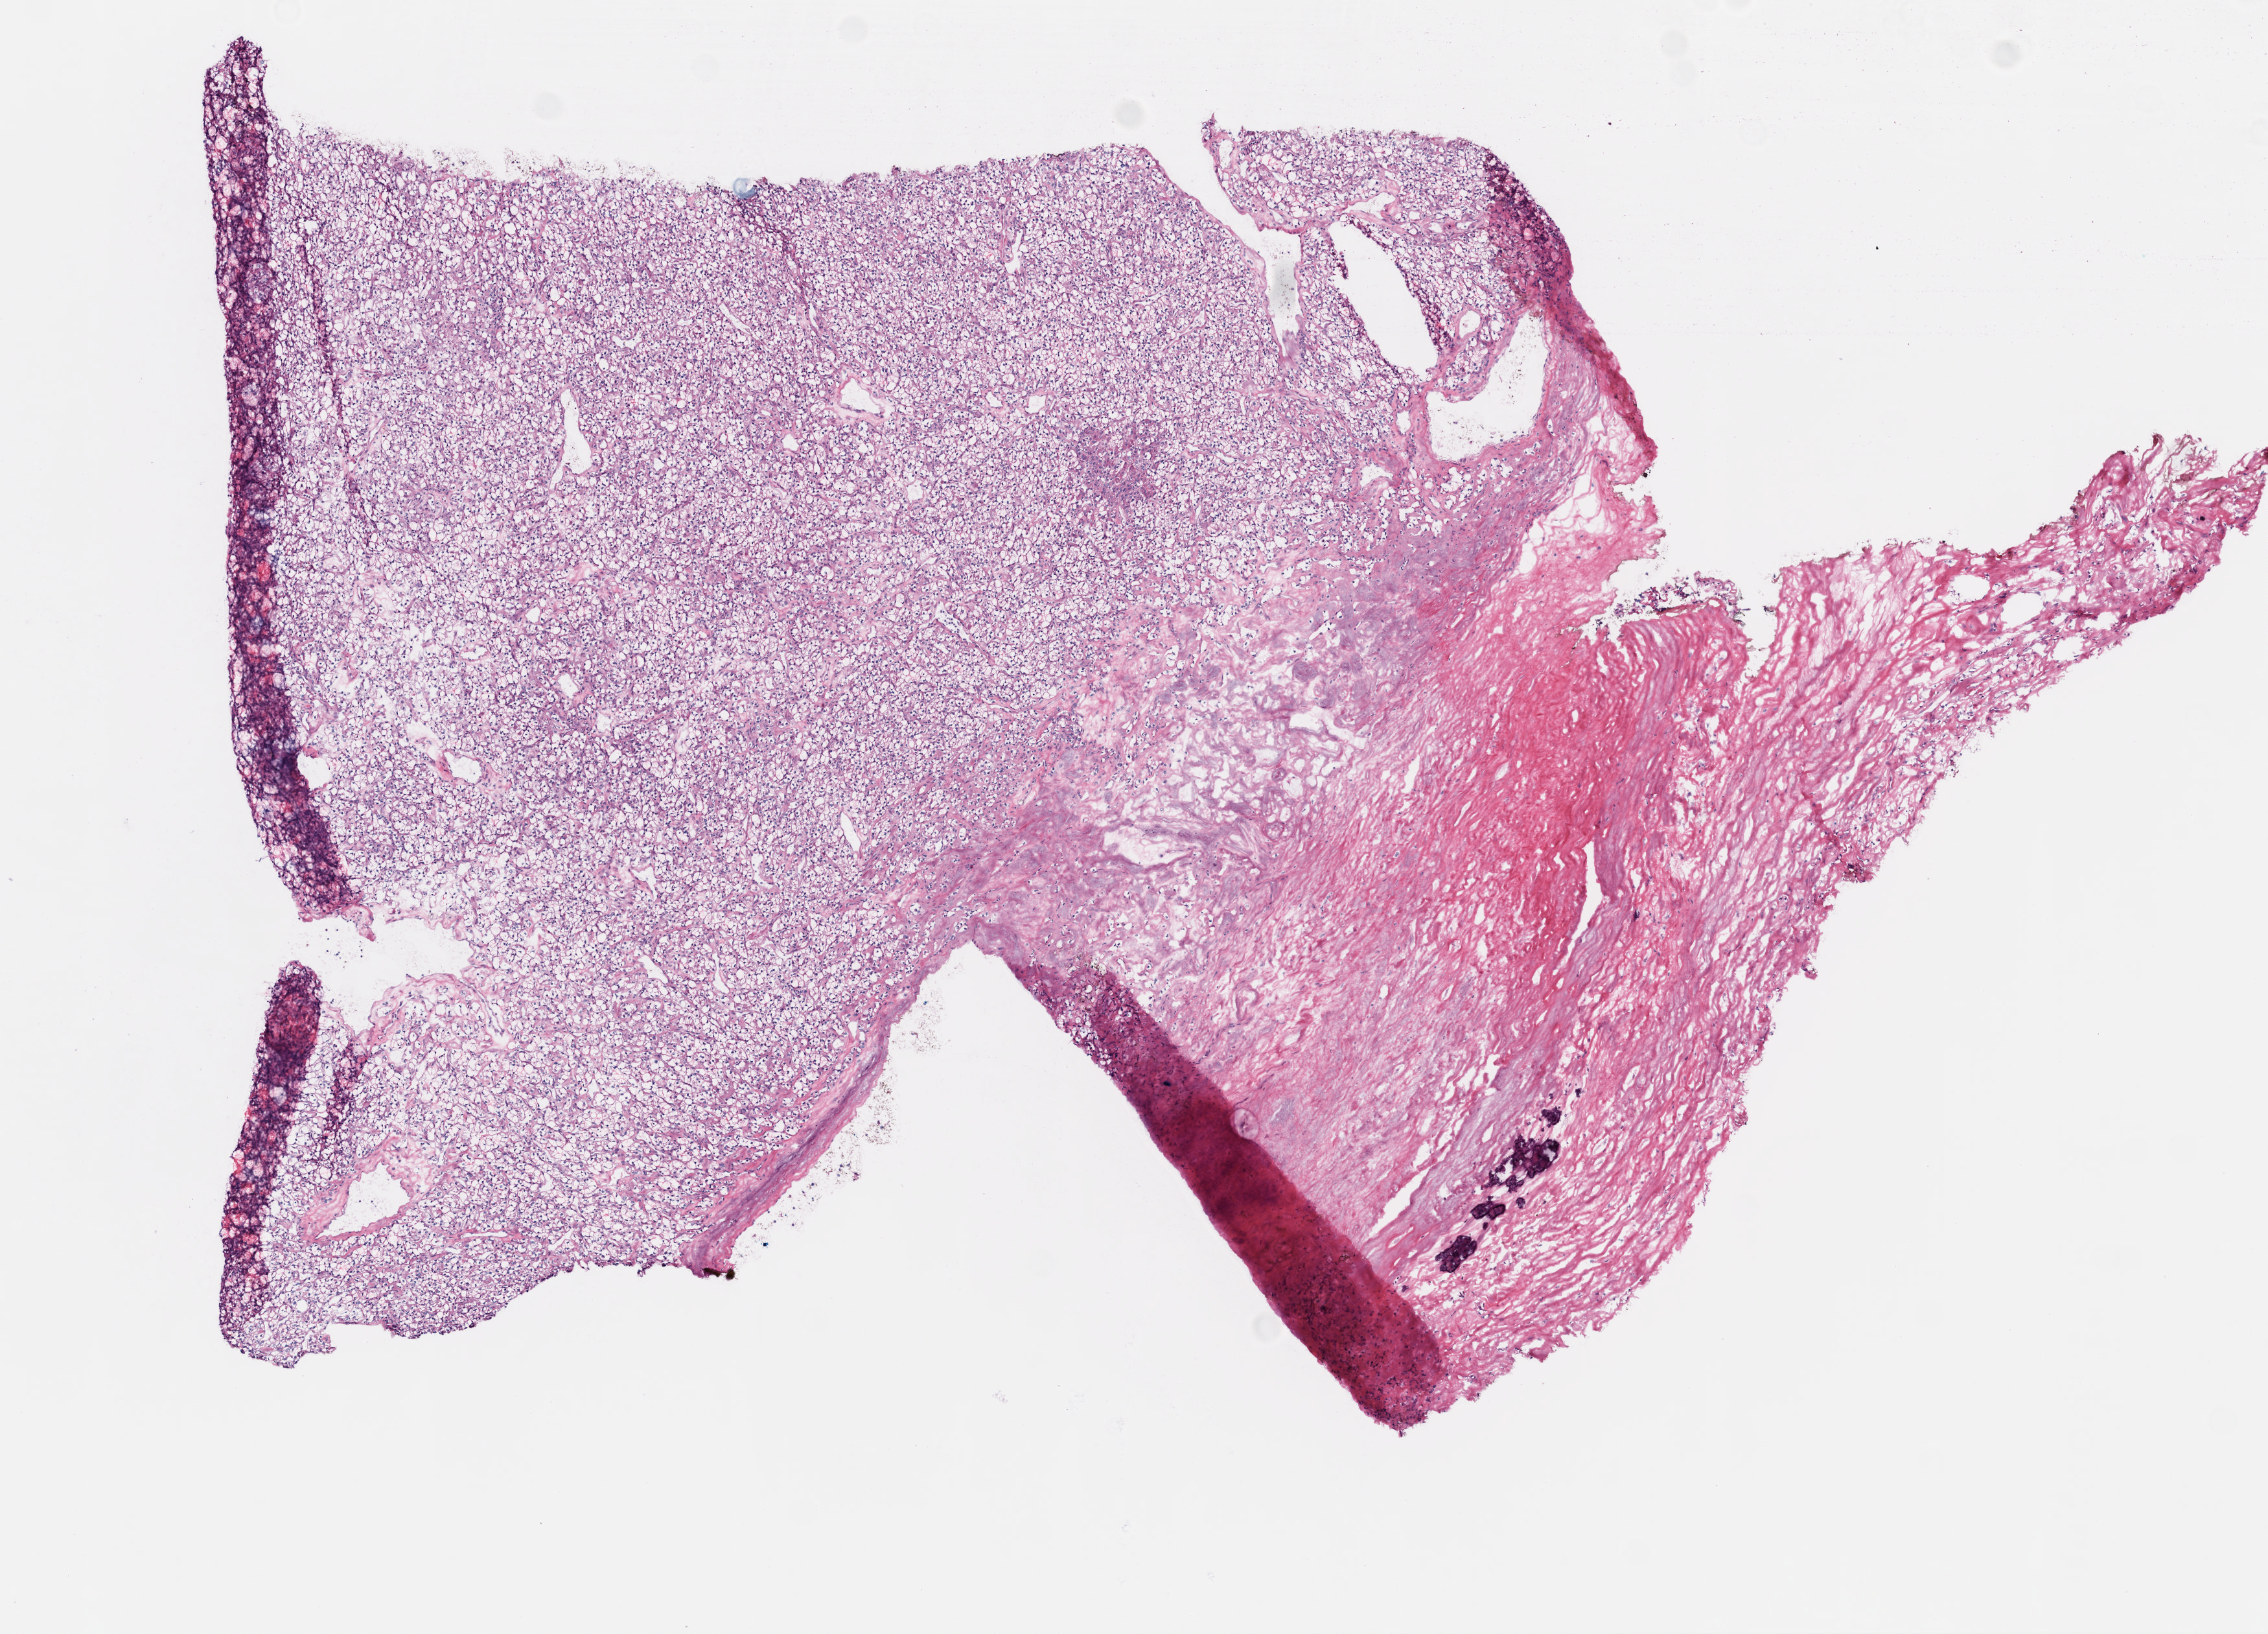
H&E-stained whole-slide image, shown as a low-resolution overview of the whole scanned area (about 7.0 x 5.1 mm), frozen section, primary tumour sample from the kidney. Patient: male, age at initial diagnosis 74 years. Histologic grade: G3 (poorly differentiated). Composition of this section per pathologist review: tumour cells 70%, tumour nuclei 85%, normal cells 0%, stromal cells 30%, necrosis 0%.
- AJCC pathologic stage: III
- pathologic diagnosis: Clear cell adenocarcinoma, NOS
- laterality: left